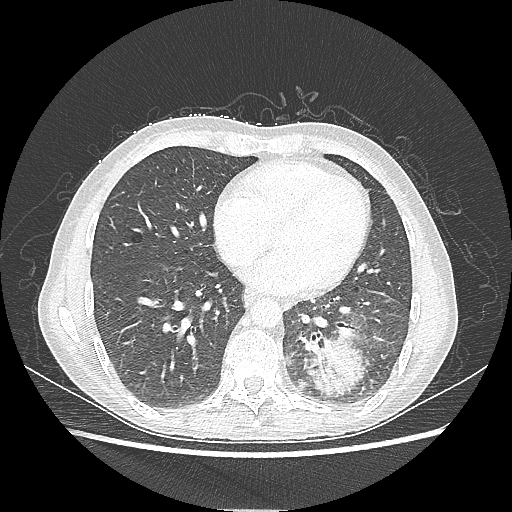
Chest CT, one axial slice; slice 86 of 220 in the series (ordered by position); 80 kVp; lung window (W 1500 / L -600 HU); 1.25 mm slice thickness; 512 × 512 image matrix. Female patient, age 53 years. Case-level facts recorded for this patient, not image findings: clinical TNM (as recorded): T3 N0 M0.
Outlined on this slice (rectangle marked by the reading radiologist):
- lung tumour (recorded histology: adenocarcinoma): bounding box (x1, y1, x2, y2) in pixels: (298, 326, 370, 397)